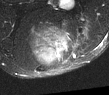
MRI of an extremity soft-tissue mass, one axial slice; slice 37 of 52 in the series (ordered by position); T2-weighted fat-saturated; MR volume resampled by the dataset authors to the PET/CT grid (not the native acquisition matrix); 3.27 mm slice thickness; 109 × 95 image matrix, field of view 106 × 93 mm. Male patient. From the clinical record (not read from this slice): histological type: synovial sarcoma; site of the primary tumour: left poplietal fossa.
Outlined on this slice (expert contour drawn on MRI and transferred to this co-registered scan by the dataset authors):
- gross tumour volume (mass): bounding box (x1, y1, x2, y2) in pixels: (33, 28, 66, 66)